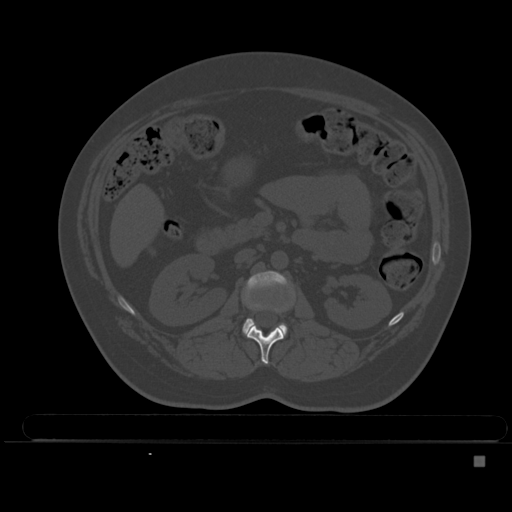
CT including the spine, one axial slice. Position 185 of 495 along the scan axis. Bone window (W 1800 / L 400 HU). 512 × 512 image matrix, field of view 404 × 404 mm. Female patient, age 33 years. From the clinical record (not read from this slice): primary cancer: breast.
Annotated regions visible in this slice (semi-automatic segmentation, software-assisted and operator-edited):
- L1 vertebra: box from (x=246, y=286) to (x=293, y=364) px
- L2 vertebra: (x=242, y=270)–(x=289, y=336)